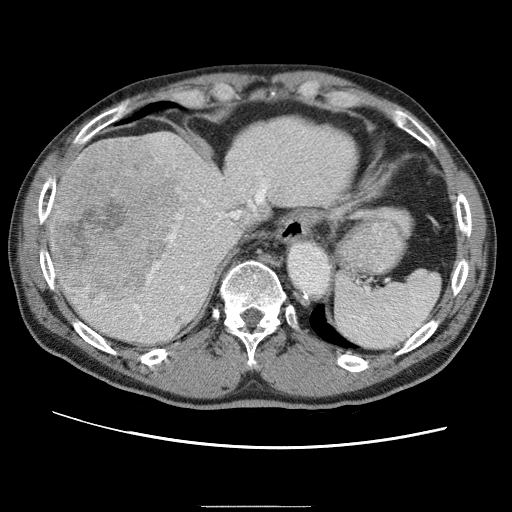
Contrast-enhanced abdominal CT (liver protocol), one axial slice. Position 51 of 75 along the scan axis. Reconstruction kernel STANDARD. 120 kVp. One of 2 acquisitions stored at this slice position. Soft-tissue window (W 400 / L 40 HU). 2.5 mm slice thickness. 512 × 512 image matrix, field of view 360 × 360 mm. Case-level facts recorded for this patient, not image findings: diagnosis: hepatocellular carcinoma (patient treated with transarterial chemoembolisation; whether this scan precedes or follows treatment is not stated here); TNM stage (as recorded): Stage-II; Child-Pugh class: A; tumour differentiation: well differentiated.
Structures marked on this image (semi-automatic segmentation, software-assisted and operator-edited):
- abdominal aorta: bounding box (x1, y1, x2, y2) in pixels: (287, 242, 329, 296)
- liver parenchyma outside the tumour (the mass and vessels are separate outlines, so this box may not span the whole liver): (49, 116, 361, 344)
- mass: (52, 142, 187, 303)
- liver vessels: (121, 140, 320, 310)